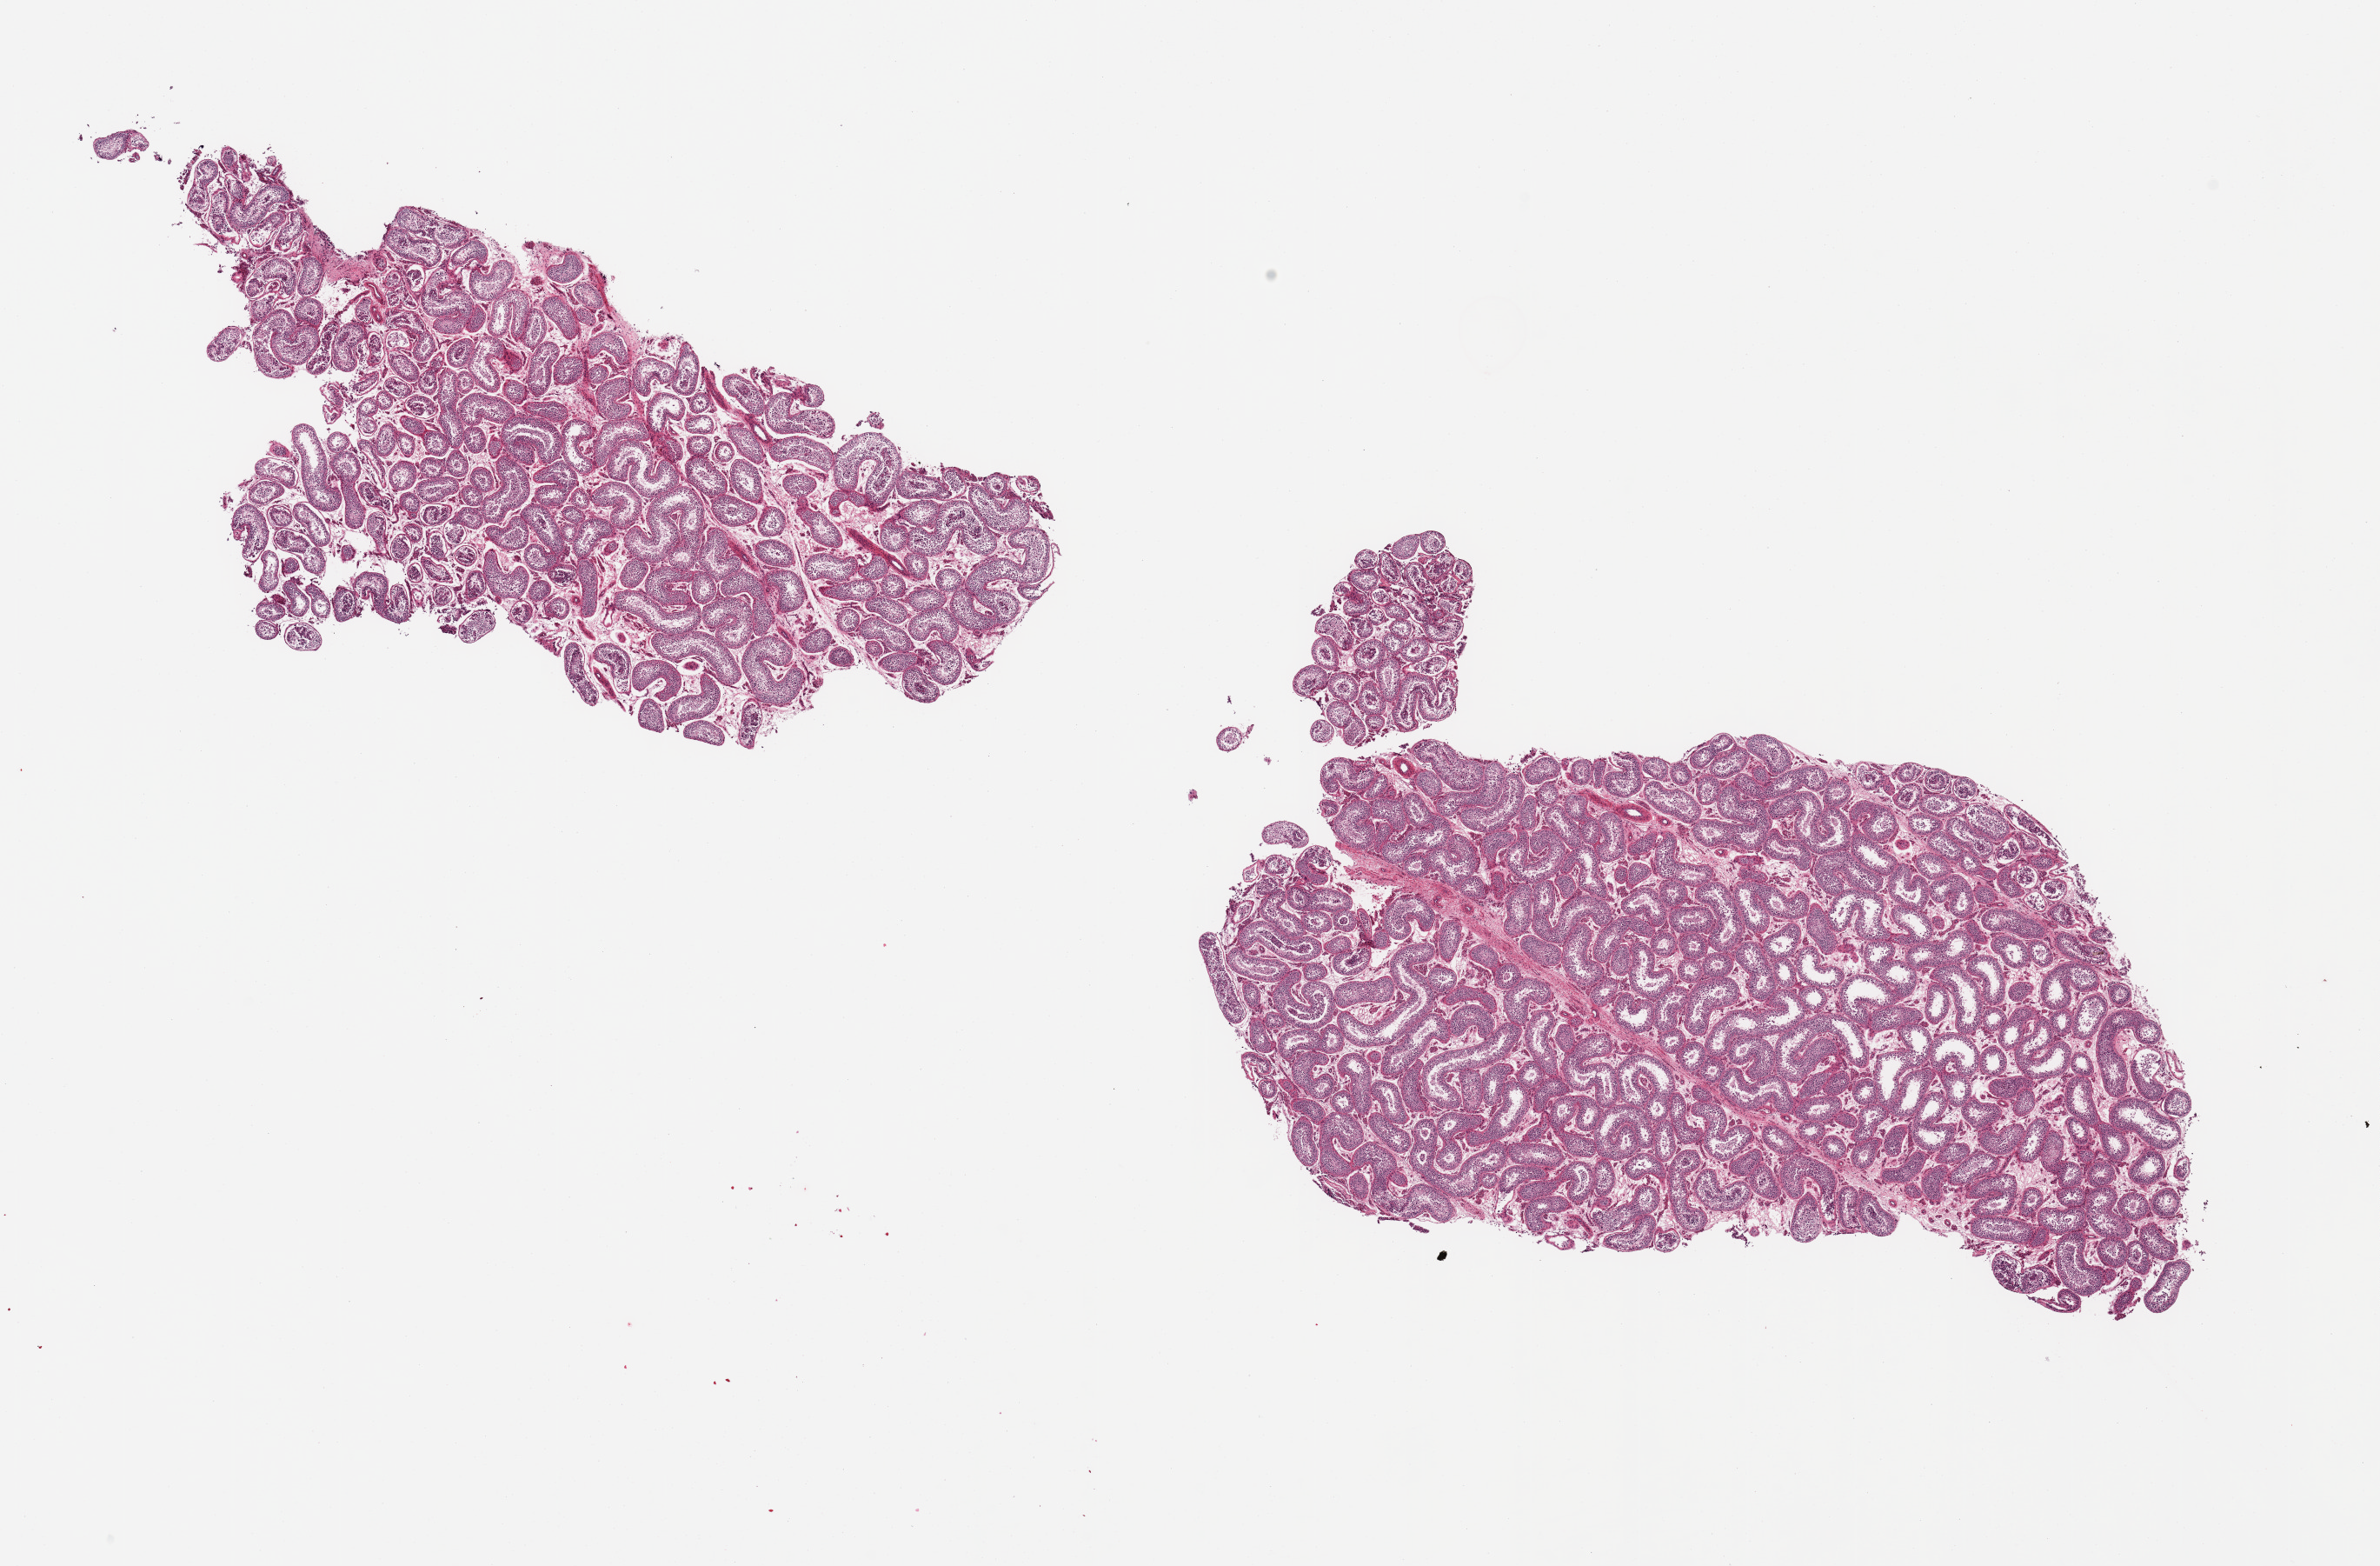
Digitized haematoxylin and eosin-stained section, brightfield, low-resolution overview of the scanned area, about 21.7 x 14.2 mm (acquisition: 20x scan); PAXgene-fixed, paraffin-embedded tissue; section of testis (target tissue); donor tissue sample. Donor sex: male.
• pathologist's review note for this sample: 2 pieces, spermatogenesis is present